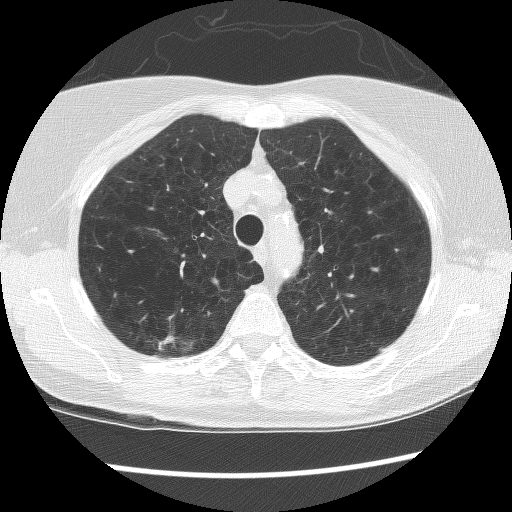
Axial slice from a low-dose chest CT screening exam; second screening round (one year after baseline); lung window (W 1500 / L -600 HU); lung (sharp) reconstruction kernel (BONE); 120 kVp; slice 30 of 134 in the series. Female, age 63 years at enrolment.
Lesion marked by an expert reader, bounding box [x1, y1, x2, y2] px = [135, 317, 202, 372]. Screening reader's record for this exam (one nodule recorded; not confirmed to be the boxed lesion): non-calcified nodule or mass ≥4 mm, right upper lobe, 16 × 7 mm, spiculated (stellate) margins, mixed attenuation, pre-existing on the prior screen: yes; interval growth: yes. Official screen result: positive, other. Lung cancer was diagnosed 43 days after this screen: bronchiolo-alveolar carcinoma, non-mucinous, right upper lobe, well differentiated (G1), stage IA (AJCC 6th edition), 12 mm at pathology.